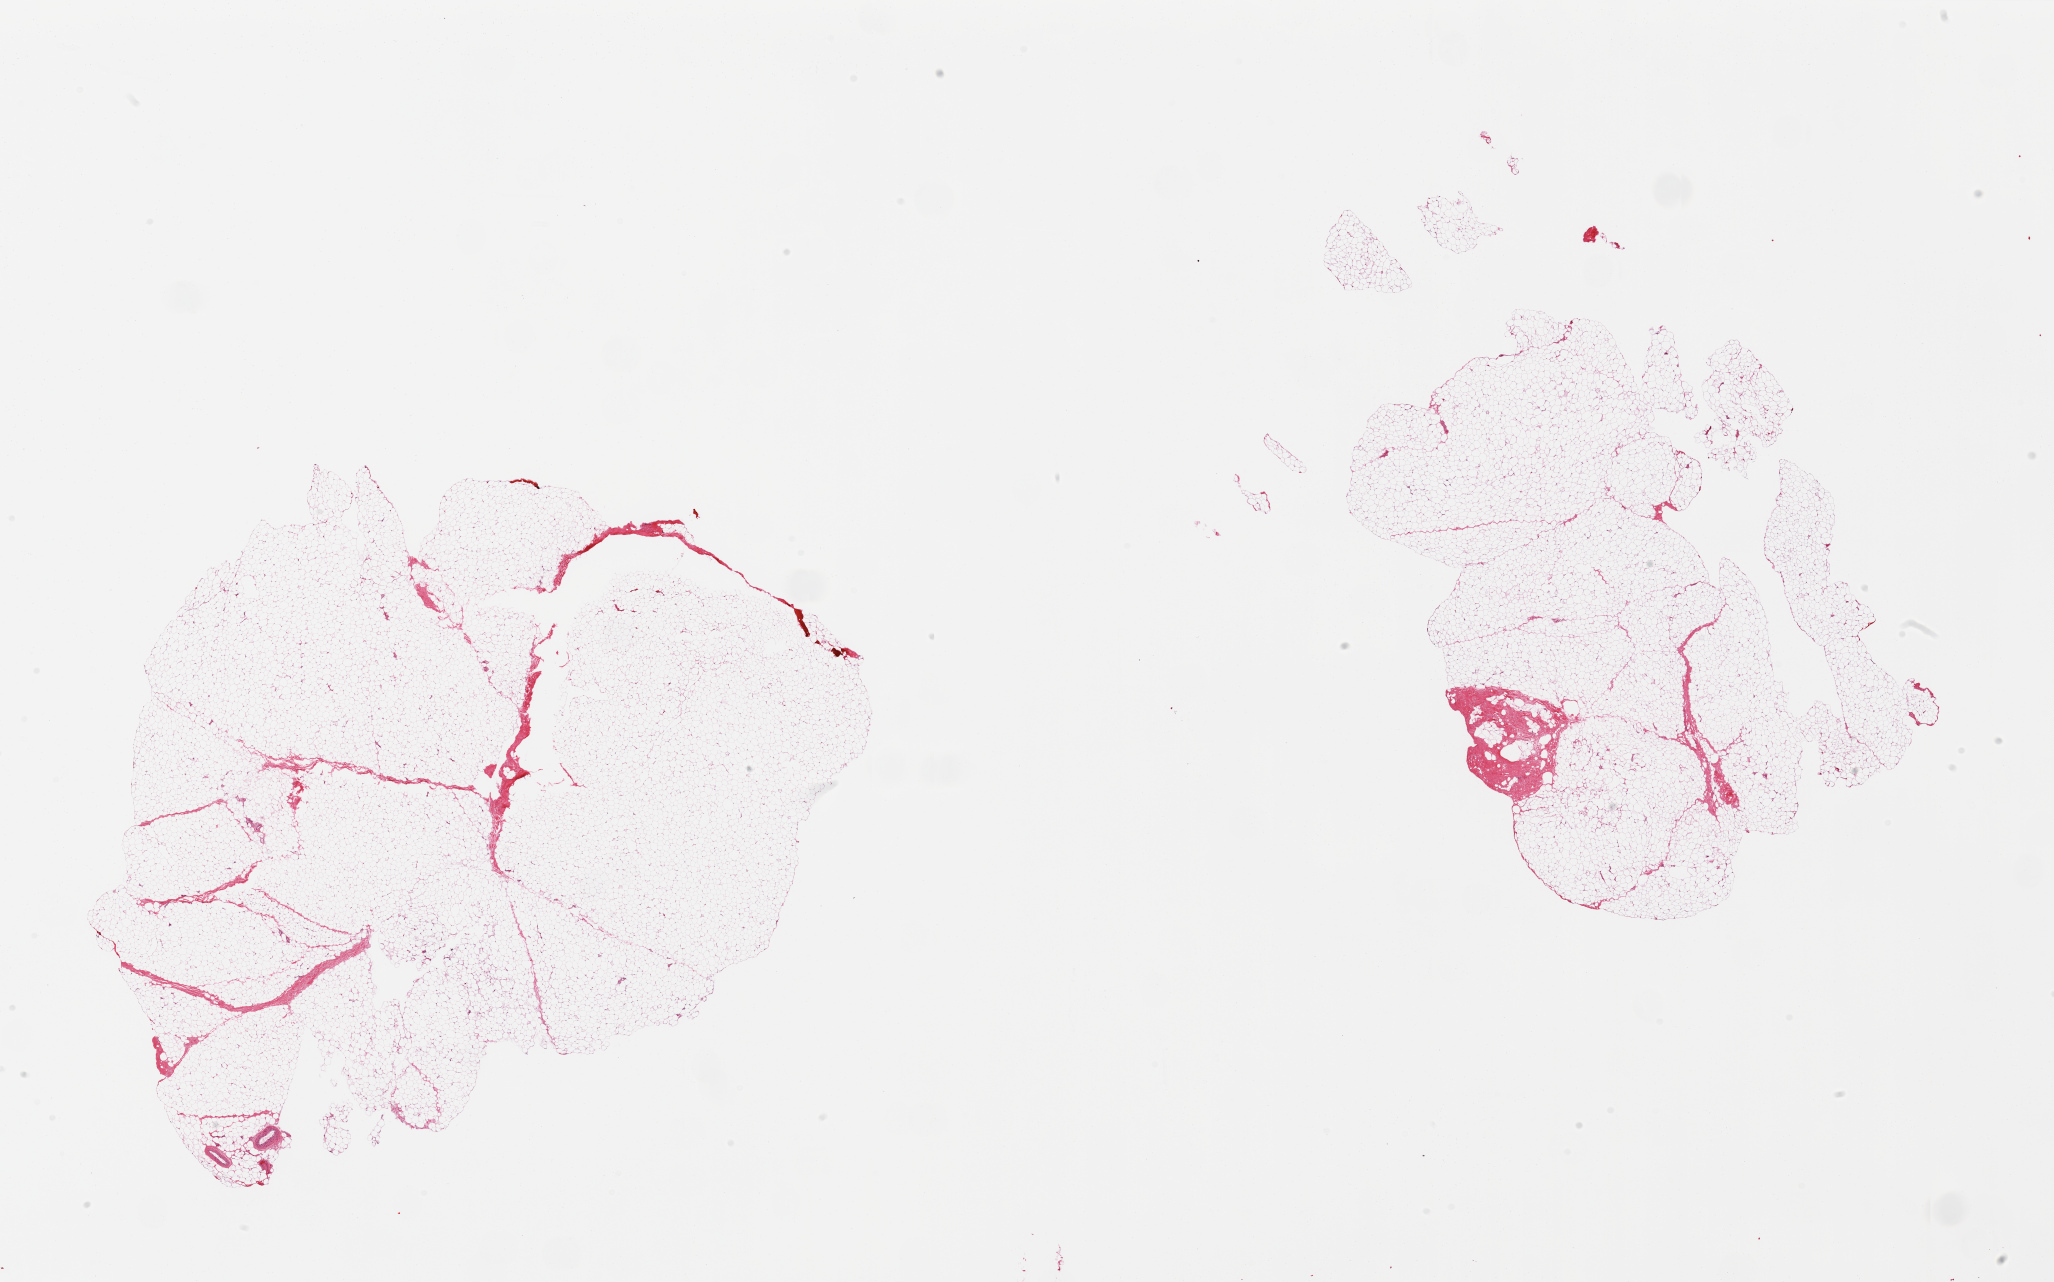
Haematoxylin and eosin whole-slide image, whole scanned area (about 32.5 x 20.3 mm, slide scanned at 20x) shown as a low-resolution overview, PAXgene-fixed paraffin-embedded (PFPE) section, target tissue: breast, tissue donor sample.
Review note (as recorded): 2 pieces, mainly adipose with ~10% fibrous tissue; no ductal elements.